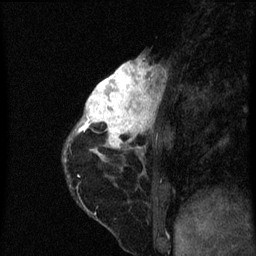
Breast MRI (dynamic contrast-enhanced), one sagittal slice; dynamic contrast-enhanced series, image 2 of 3 at this slice position (ordered by acquisition); 1.5 T; TE 4.2 ms, TR 8 ms; 2 mm slice thickness; 256 × 256 image matrix. Patient: female, 38 years.
Structures marked on this image (semi-automatically segmented with operator editing):
- analysis volume of interest (the breast-tissue region the enhancement analysis was run in; not a lesion): bounding box <80,60,165,151> (left, top, right, bottom; pixels)
- tumour enhancement mask (voxels above the 70 % enhancement threshold inside the analysis volume of interest): <80,60,159,149>